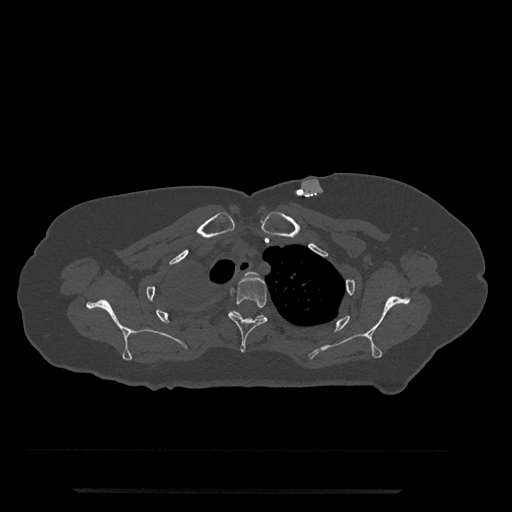
CT including the spine, one axial slice. Reconstruction kernel Br40s/3. Bone window (W 1800 / L 400 HU). 512 × 512 image matrix, field of view 440 × 440 mm. Patient: female, 51 years. From the clinical record (not read from this slice): primary cancer: neuro; vertebrae with lytic lesions (as recorded): T8.
Structures marked on this image (semi-automatic segmentation, software-assisted and operator-edited):
- T2 vertebra: box from (x=246, y=273) to (x=249, y=275) px
- T3 vertebra: (x=228, y=273)–(x=268, y=353)
- T4 vertebra: (x=232, y=311)–(x=265, y=319)